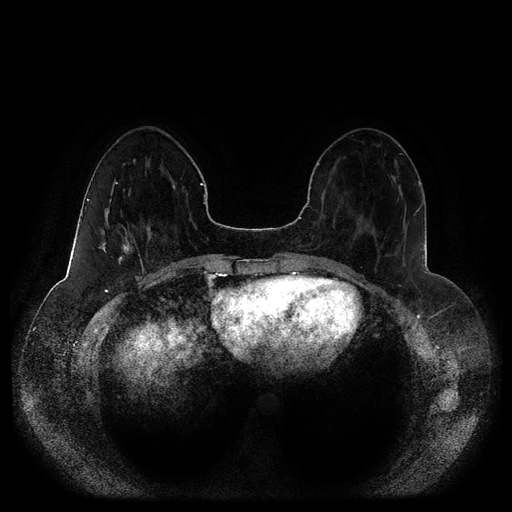
Breast MRI (dynamic contrast-enhanced, multi-phase), one axial slice. Position 35 of 116 along the scan axis. Dynamic contrast-enhanced series, time point 2 of 5 at this slice position (early post-contrast). 1.5 T. TE 2.5 ms, TR 5.2 ms. 2 mm slice thickness. 512 × 512 image matrix. Female patient, age 44 years.
Structures marked on this image (semi-automatically segmented with operator editing):
- breast lesion (labelled 'tumour' in the annotation; benign lesions carry a separate 'benign' label): bounding box [x1, y1, x2, y2] px = [99, 182, 131, 273]